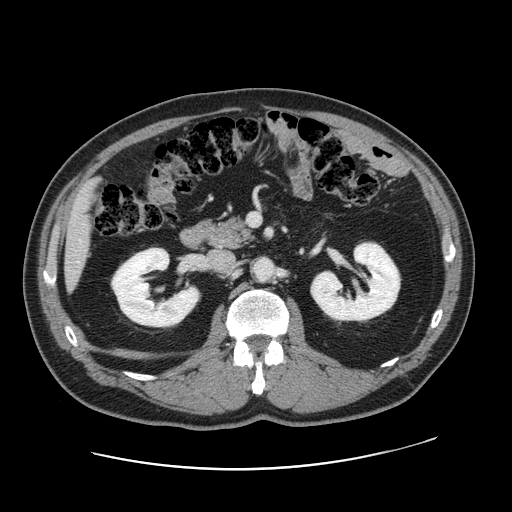
Contrast-enhanced abdominal CT, one axial slice. Intravenous contrast given. Soft-tissue window (W 400 / L 40 HU). 512 × 512 image matrix, field of view 403 × 403 mm. Male patient, age 63 years. Case-level facts recorded for this patient, not image findings: diagnosis: colorectal cancer liver metastases, imaged before liver resection; multiple liver metastases: yes; largest metastasis: 8 cm; disease in both lobes: yes.
Structures marked on this image (outlined manually by an expert reader):
- liver: bounding box <66,185,95,283> (left, top, right, bottom; pixels)